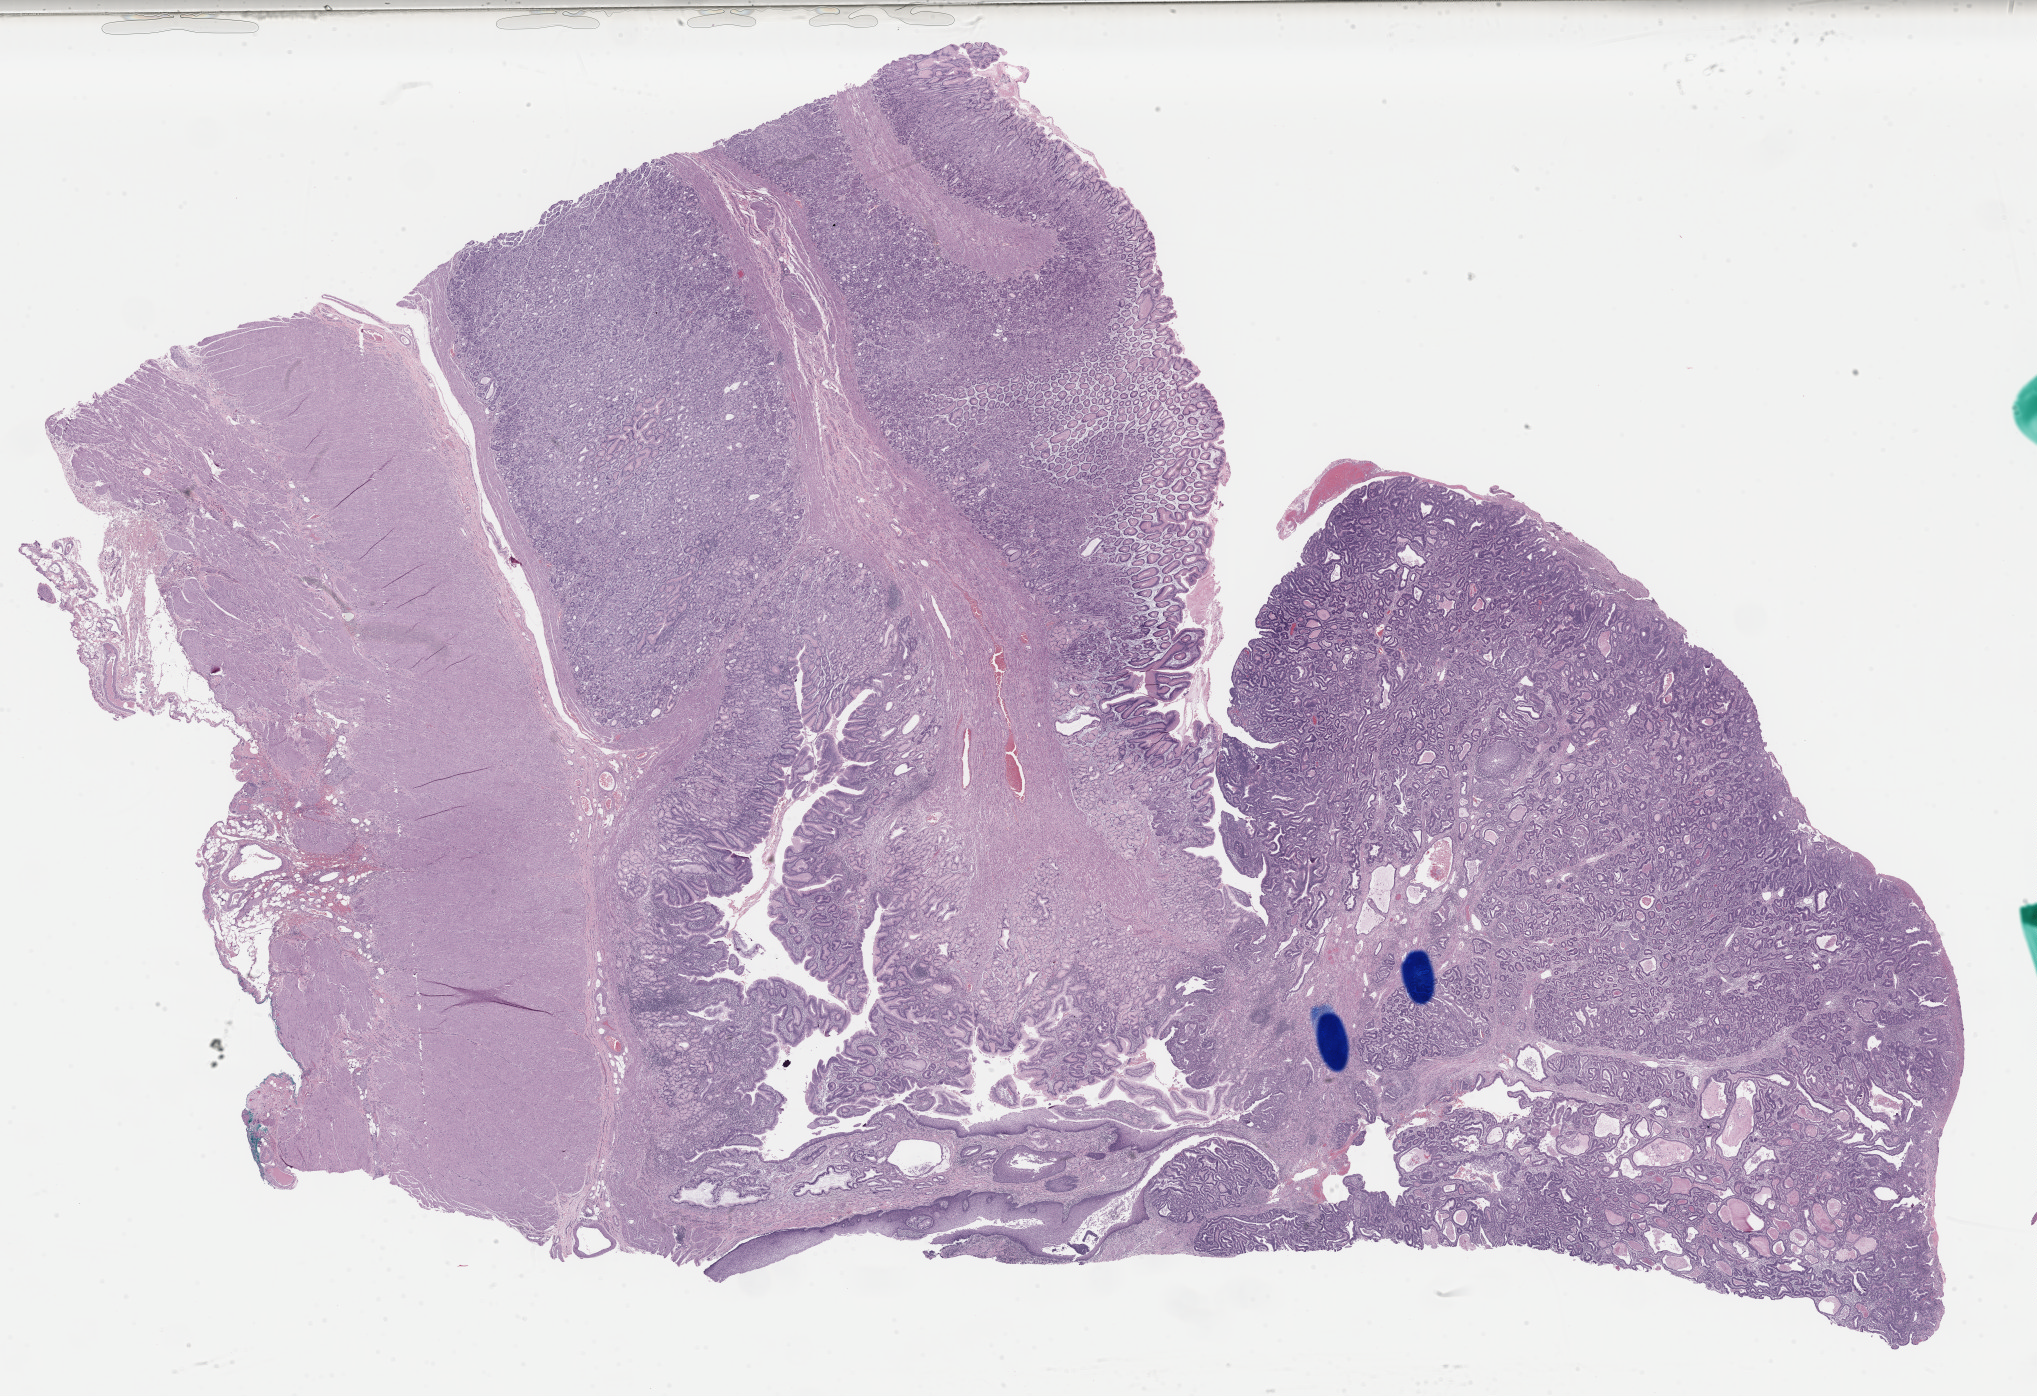
Hematoxylin and eosin (H&E) stained whole-slide image, whole scanned area (about 32.1 x 22.0 mm, slide scanned at 40x) shown as a low-resolution overview, formalin-fixed paraffin-embedded (FFPE) diagnostic section, primary tumour sample from the esophagus. Patient: female, age at initial diagnosis 67 years.
Diagnosis: Adenocarcinoma, NOS (lower third of esophagus).